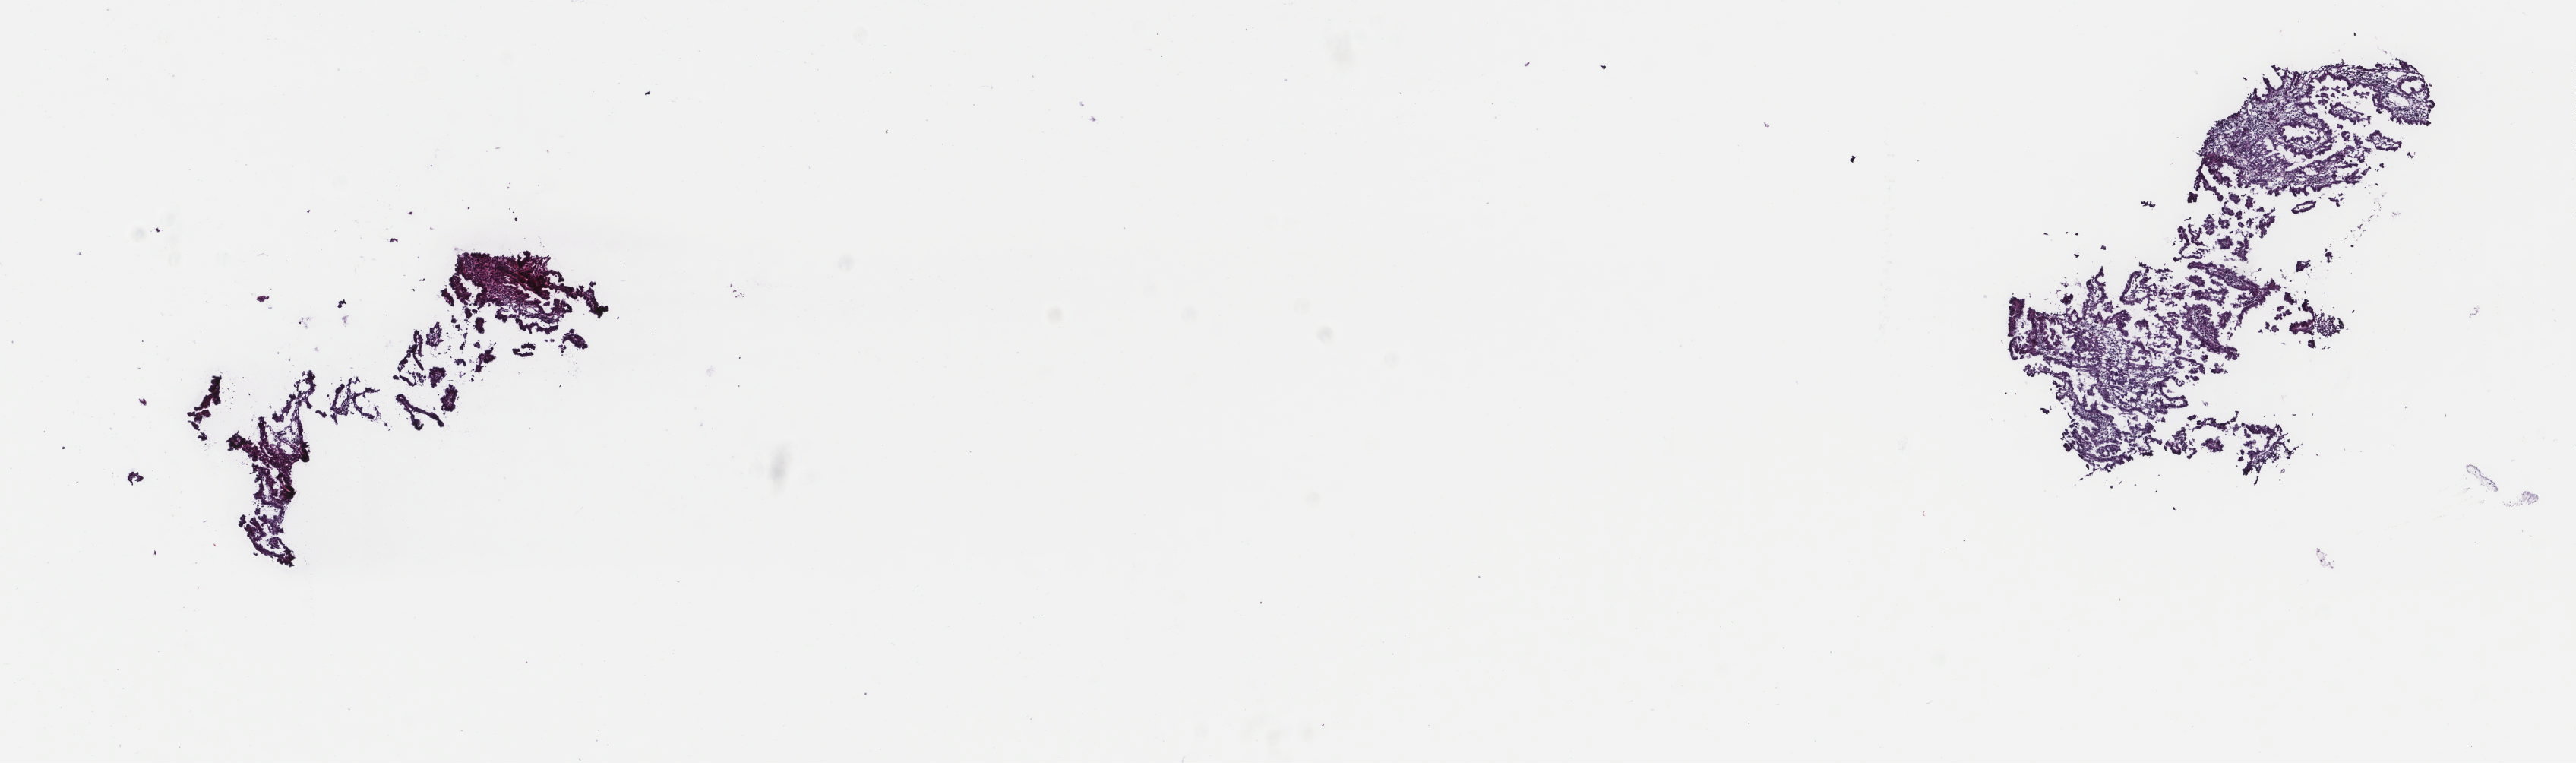
Hematoxylin and eosin (H&E) stained whole-slide image, whole scanned area (about 13.5 x 4.0 mm) shown as a low-resolution overview, frozen section from the top of the tissue portion, sample: primary tumour, uterus. Female patient; age at initial diagnosis 61 years. Histologic grade: G3 (poorly differentiated). Composition of this section per pathologist review: tumour cells 100%, tumour nuclei 60%, normal cells 0%, stromal cells 0%, necrosis 0%. Infiltration values recorded for this section: lymphocyte infiltration 0%, monocyte infiltration 0%, neutrophil infiltration 0%.
Pathologic diagnosis: Serous cystadenocarcinoma, NOS (endometrium). Lymph nodes positive (case pathology): 0 of 18 examined. FIGO stage: IA.